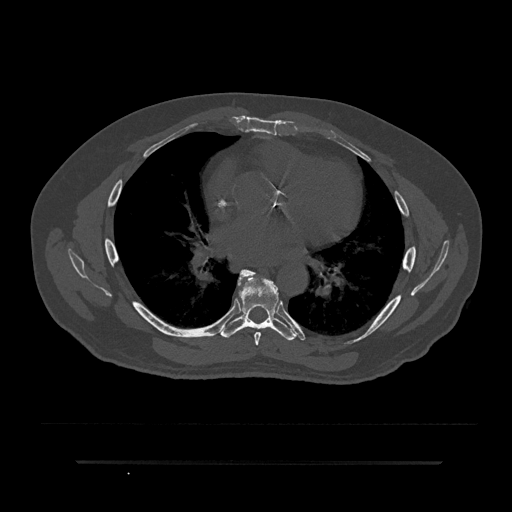
CT including the spine, one axial slice. Bone window (W 1800 / L 400 HU). 0.5 mm slice thickness. 512 × 512 image matrix, field of view 464 × 464 mm. Patient: male, 59 years. From the clinical record (not read from this slice): primary cancer: bile ducts; vertebrae with lytic lesions (as recorded): T10.
Structures marked on this image (semi-automatically segmented with operator editing):
- T6 vertebra: box from (x=238, y=272) to (x=261, y=346) px
- T7 vertebra: (x=220, y=269)–(x=296, y=341)